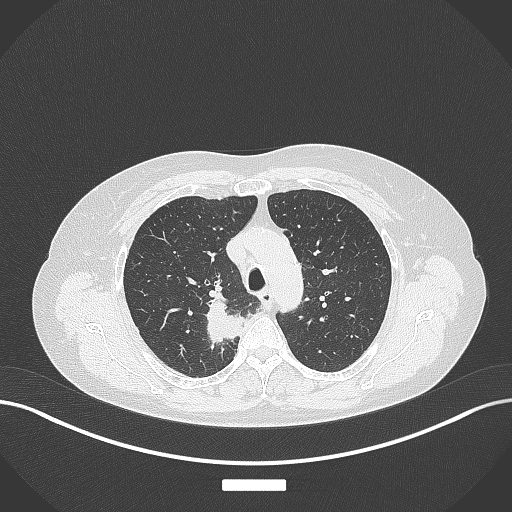
Chest CT, one axial slice; slice 286 of 357 in the series (ordered by position); 120 kVp; lung window (W 1500 / L -600 HU); 1 mm slice thickness; 512 × 512 image matrix, field of view 400 × 400 mm. Patient: female, 62 years. From the clinical record (not read from this slice): clinical TNM (as recorded): T1c N1 M0.
Outlined on this slice (rectangle marked by the reading radiologist):
- lung tumour (recorded histology: squamous cell carcinoma): bounding box (x1, y1, x2, y2) in pixels: (202, 286, 242, 343)